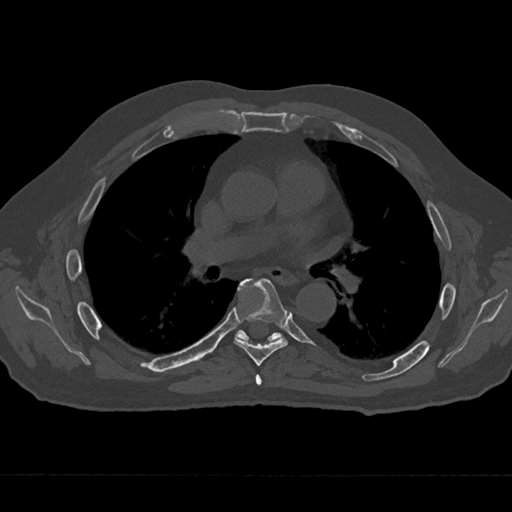
CT including the spine, one axial slice. Slice 407 of 797 in the series (ordered by position). Reconstruction kernel Br40s/3. Bone window (W 1800 / L 400 HU). 0.5 mm slice thickness. 512 × 512 image matrix. Male patient, age 75 years. Case-level facts recorded for this patient, not image findings: primary cancer: renal; vertebrae with lytic lesions (as recorded): T4.
Structures marked on this image (semi-automatic segmentation, software-assisted and operator-edited):
- T5 vertebra: bounding box [x1, y1, x2, y2] px = [255, 374, 262, 385]
- T6 vertebra: [234, 278, 288, 366]
- T7 vertebra: [236, 281, 281, 342]